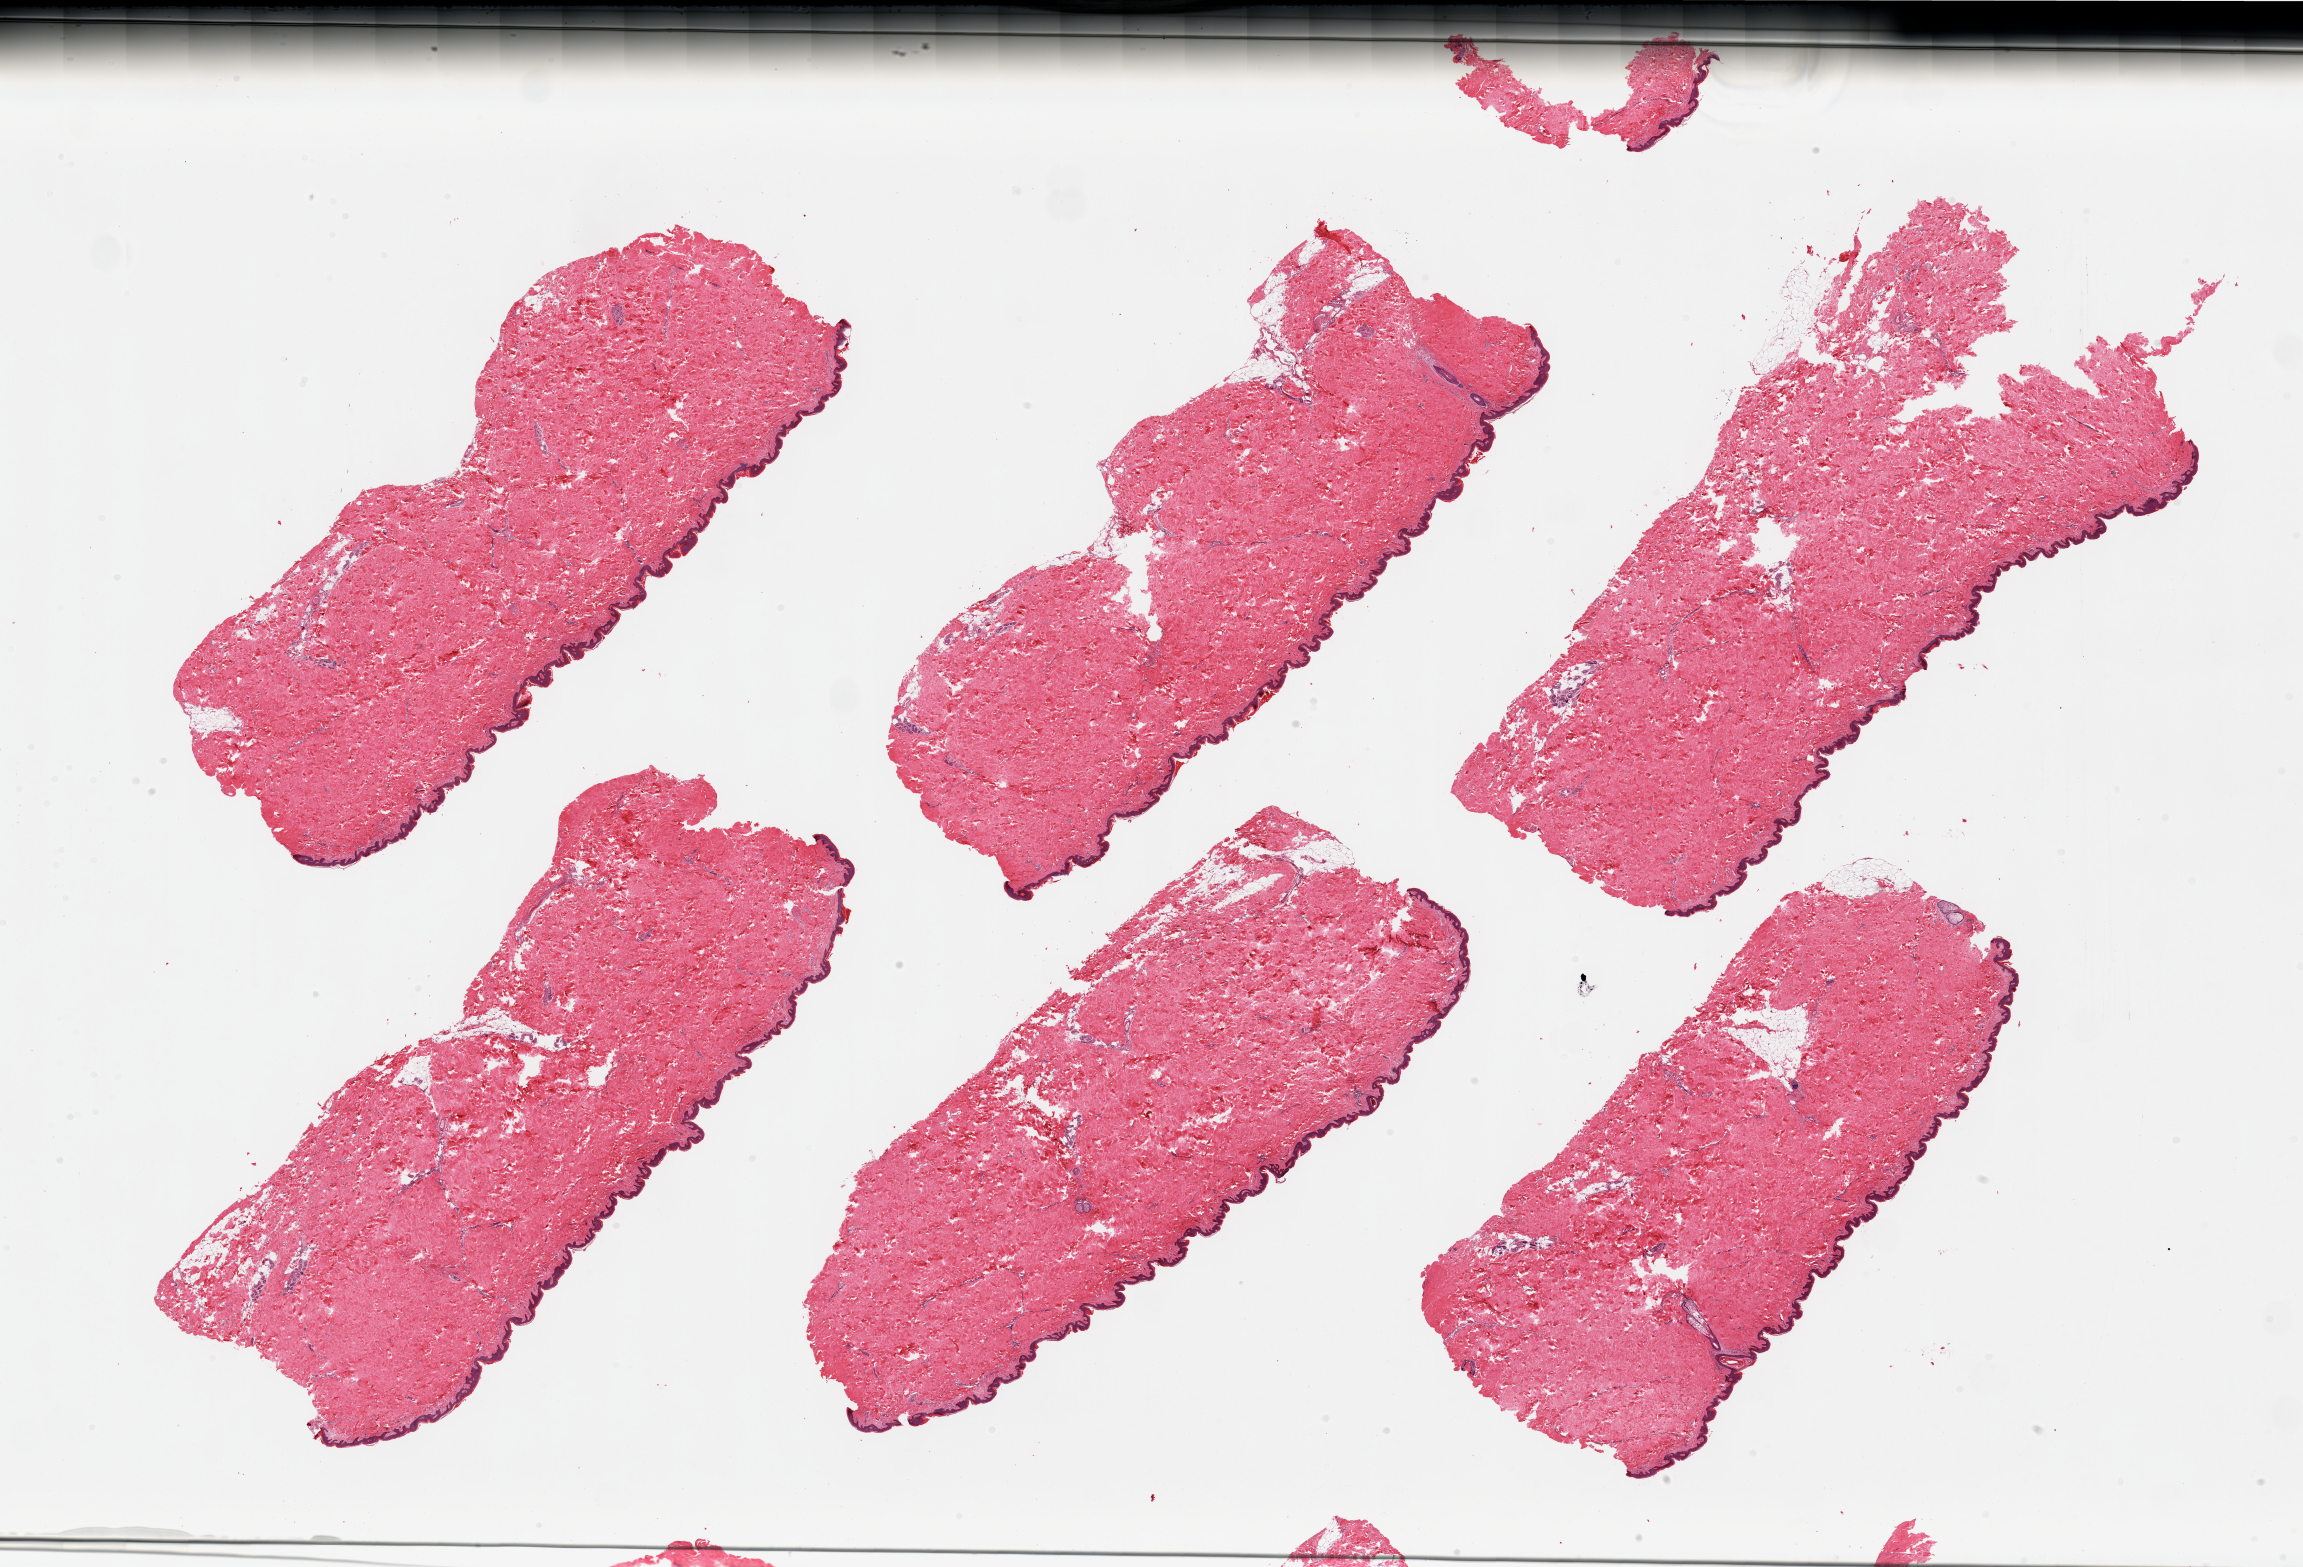
Whole-slide image, haematoxylin and eosin stain, brightfield — low-resolution overview of the scanned area, about 36.4 x 24.8 mm, PAXgene-fixed, paraffin-embedded tissue, target tissue: skin of suprapubic region, tissue donor sample. Male donor.
Reviewer comment on this tissue sample: 6 pieces; well trimmed.